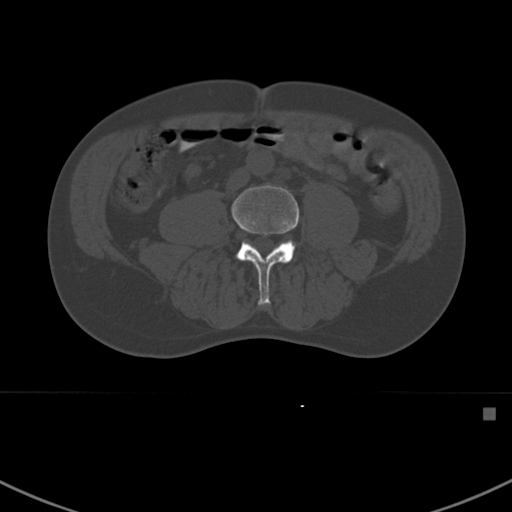
CT including the spine, one axial slice. Reconstruction kernel Br40s. Bone window (W 1800 / L 400 HU). 1.5 mm slice thickness. 512 × 512 image matrix, field of view 358 × 358 mm. Patient: male, 59 years. Case-level facts recorded for this patient, not image findings: primary cancer: prostate.
Annotated regions visible in this slice (semi-automatically segmented with operator editing):
- L4 vertebra: bounding box [x1, y1, x2, y2] px = [232, 185, 299, 306]